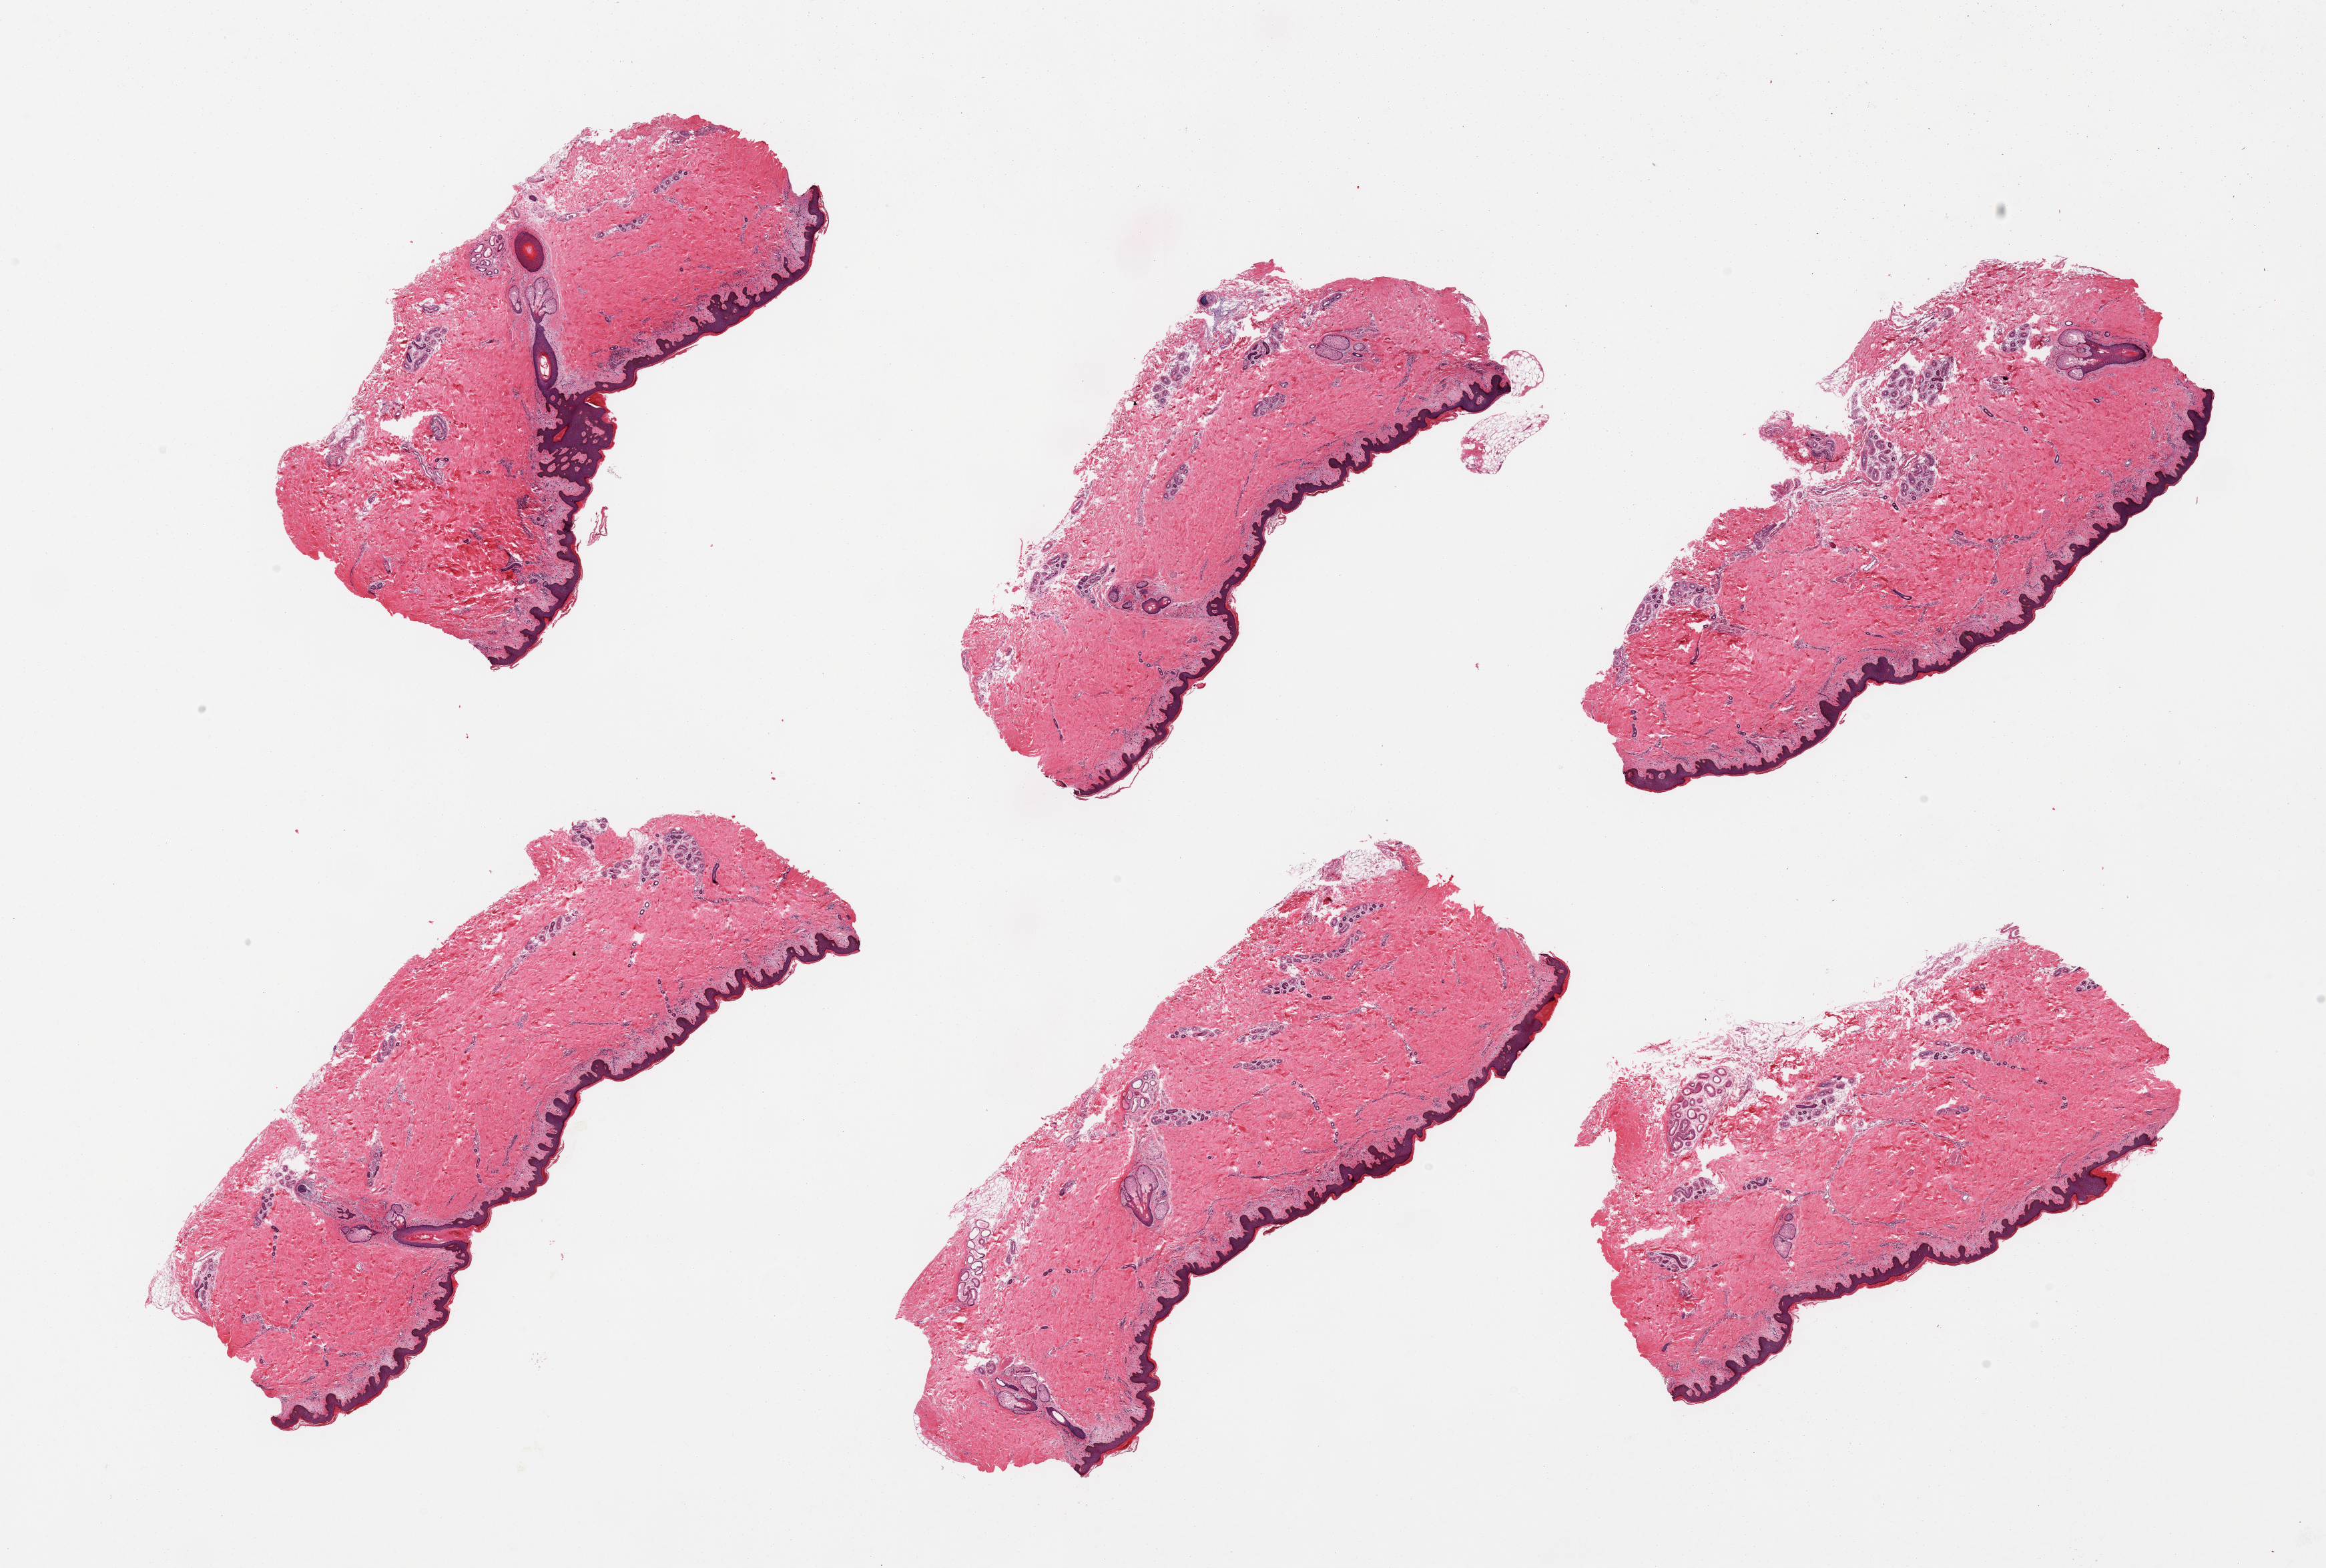
Haematoxylin and eosin whole-slide image — low-resolution overview of the scanned area, about 27.6 x 18.6 mm. PAXgene-fixed paraffin-embedded (PFPE) section. Sampled site (target tissue): skin of suprapubic region. Donor tissue sample. Male donor.
Review note (as recorded): 6 pieces; 1% dermal fat; well trimmed.